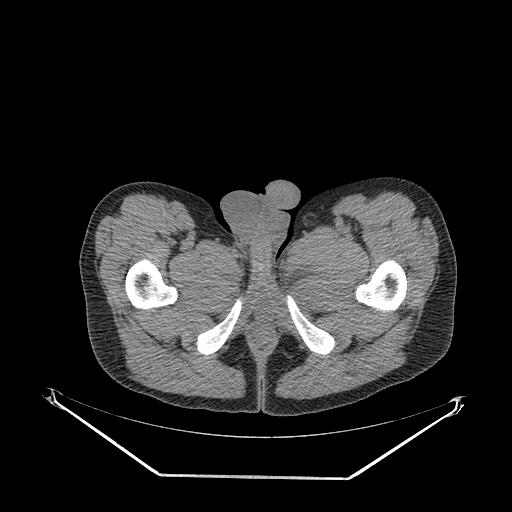
CT of an extremity soft-tissue mass (from a PET/CT study), one axial slice; position 45 of 267 along the scan axis; reconstruction kernel SOFT; 140 kVp; soft-tissue window (W 400 / L 40 HU); 512 × 512 image matrix, field of view 500 × 500 mm. Male patient. Case-level facts recorded for this patient, not image findings: histological type: pleiomorphic liposarcoma; grade: high; site of the primary tumour: left thigh.
Annotated regions visible in this slice (expert contour drawn on MRI and transferred to this co-registered scan by the dataset authors):
- gross tumour volume including surrounding oedema: bounding box [x1, y1, x2, y2] px = [288, 270, 323, 312]